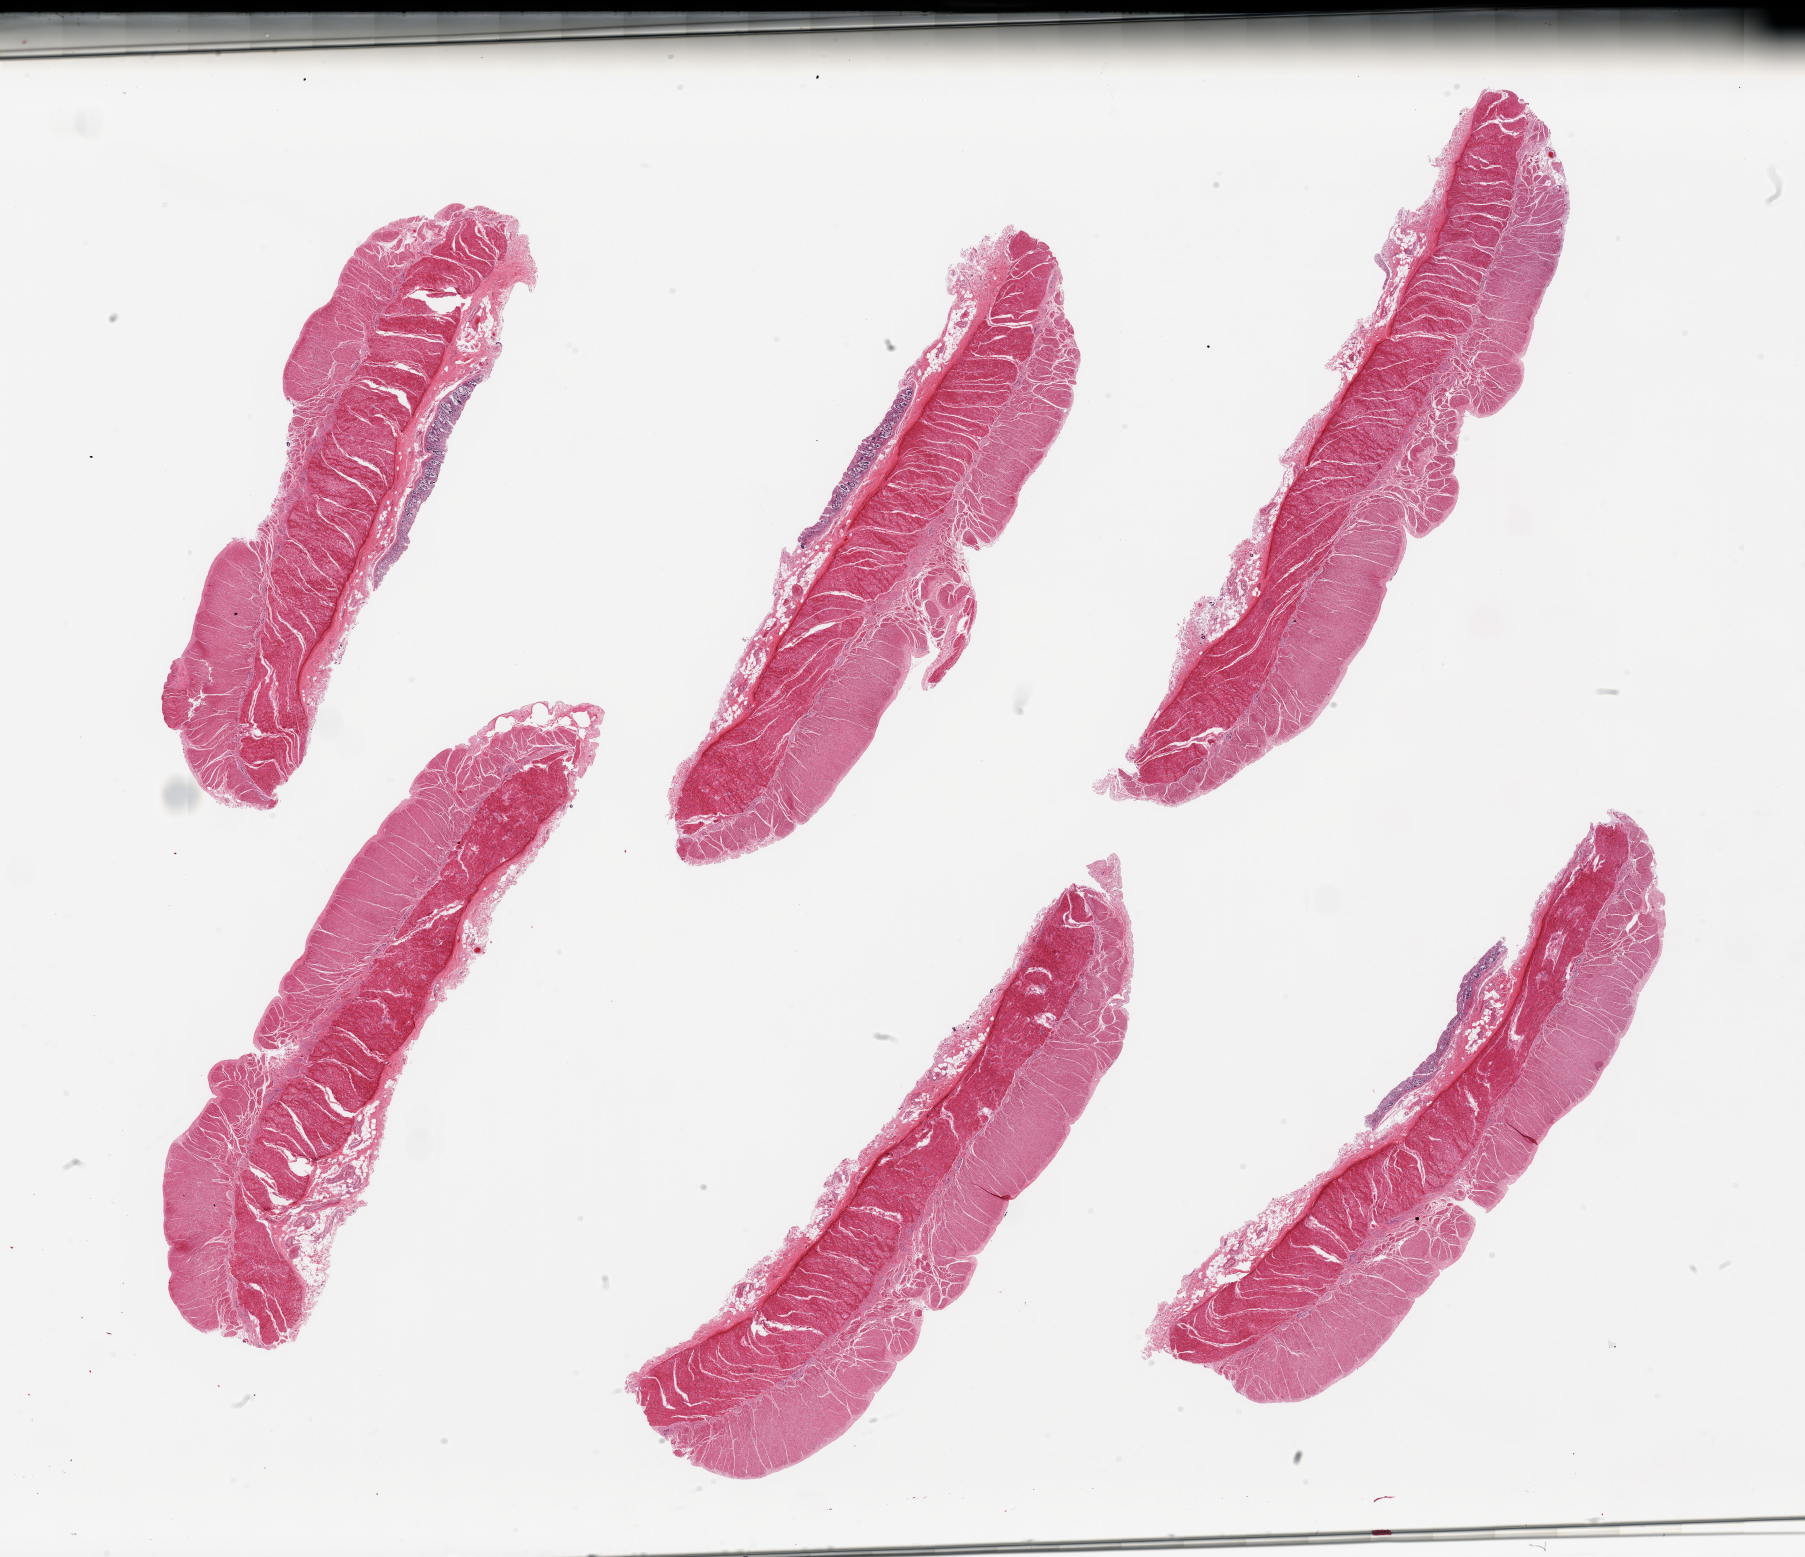
Digitized haematoxylin and eosin-stained section, brightfield — a low-resolution overview of the entire scanned area, about 28.5 x 24.6 mm, PAXgene-fixed paraffin-embedded (PFPE) section, section of sigmoid colon (target tissue), donor tissue sample. Male donor.
Review note (as recorded): 6 pieces; predominantly muscularis, some residual submucosa/mucosa.